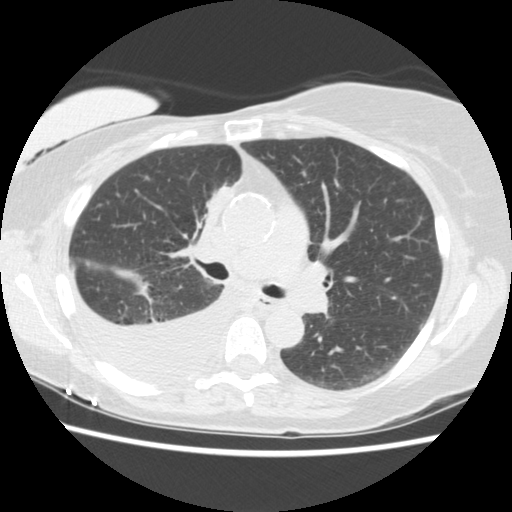
Chest CT (low-dose screening protocol), one axial image. Third annual screen. Lung window (W 1500 / L -600 HU). Standard (soft-tissue) reconstruction kernel (STANDARD). 120 kVp. Female participant, aged 56 years at enrolment. Current smoker at enrolment.
- Expert reader's lesion annotation, bounding box (x1, y1, x2, y2) in pixels: (183, 175, 246, 242).
- The screening reader recorded 2 non-calcified nodules or masses ≥4 mm on this exam; which of them this box marks is not recorded.
- Lung cancer was diagnosed 160 days after this screen: adenocarcinoma, NOS, right upper lobe, stage IIIB (AJCC 6th edition), 8 mm at pathology.